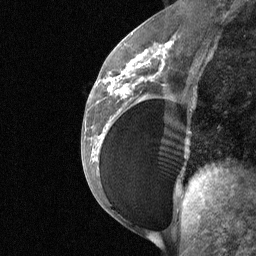
Breast MRI (dynamic contrast-enhanced), one sagittal slice; slice 33 of 64 in the series (ordered by position); dynamic contrast-enhanced study with each time point stored as its own series, time point 2 of 3 at this slice position (early post-contrast, ordered by acquisition time); 1.5 T; TE 4.8 ms, TR 27 ms; 256 × 256 image matrix. Female patient, age 34 years. From the clinical record (not read from this slice): setting: breast cancer imaged before/during neoadjuvant chemotherapy; receptor status: HR-positive, HER2-negative.
Annotated regions visible in this slice (semi-automatic segmentation, software-assisted and operator-edited):
- analysis volume of interest (the breast-tissue region the enhancement analysis was run in; not a lesion): bounding box [x1, y1, x2, y2] px = [92, 50, 188, 185]
- tumour enhancement mask (voxels above the 90 % enhancement threshold inside the analysis volume of interest): [107, 51, 164, 126]